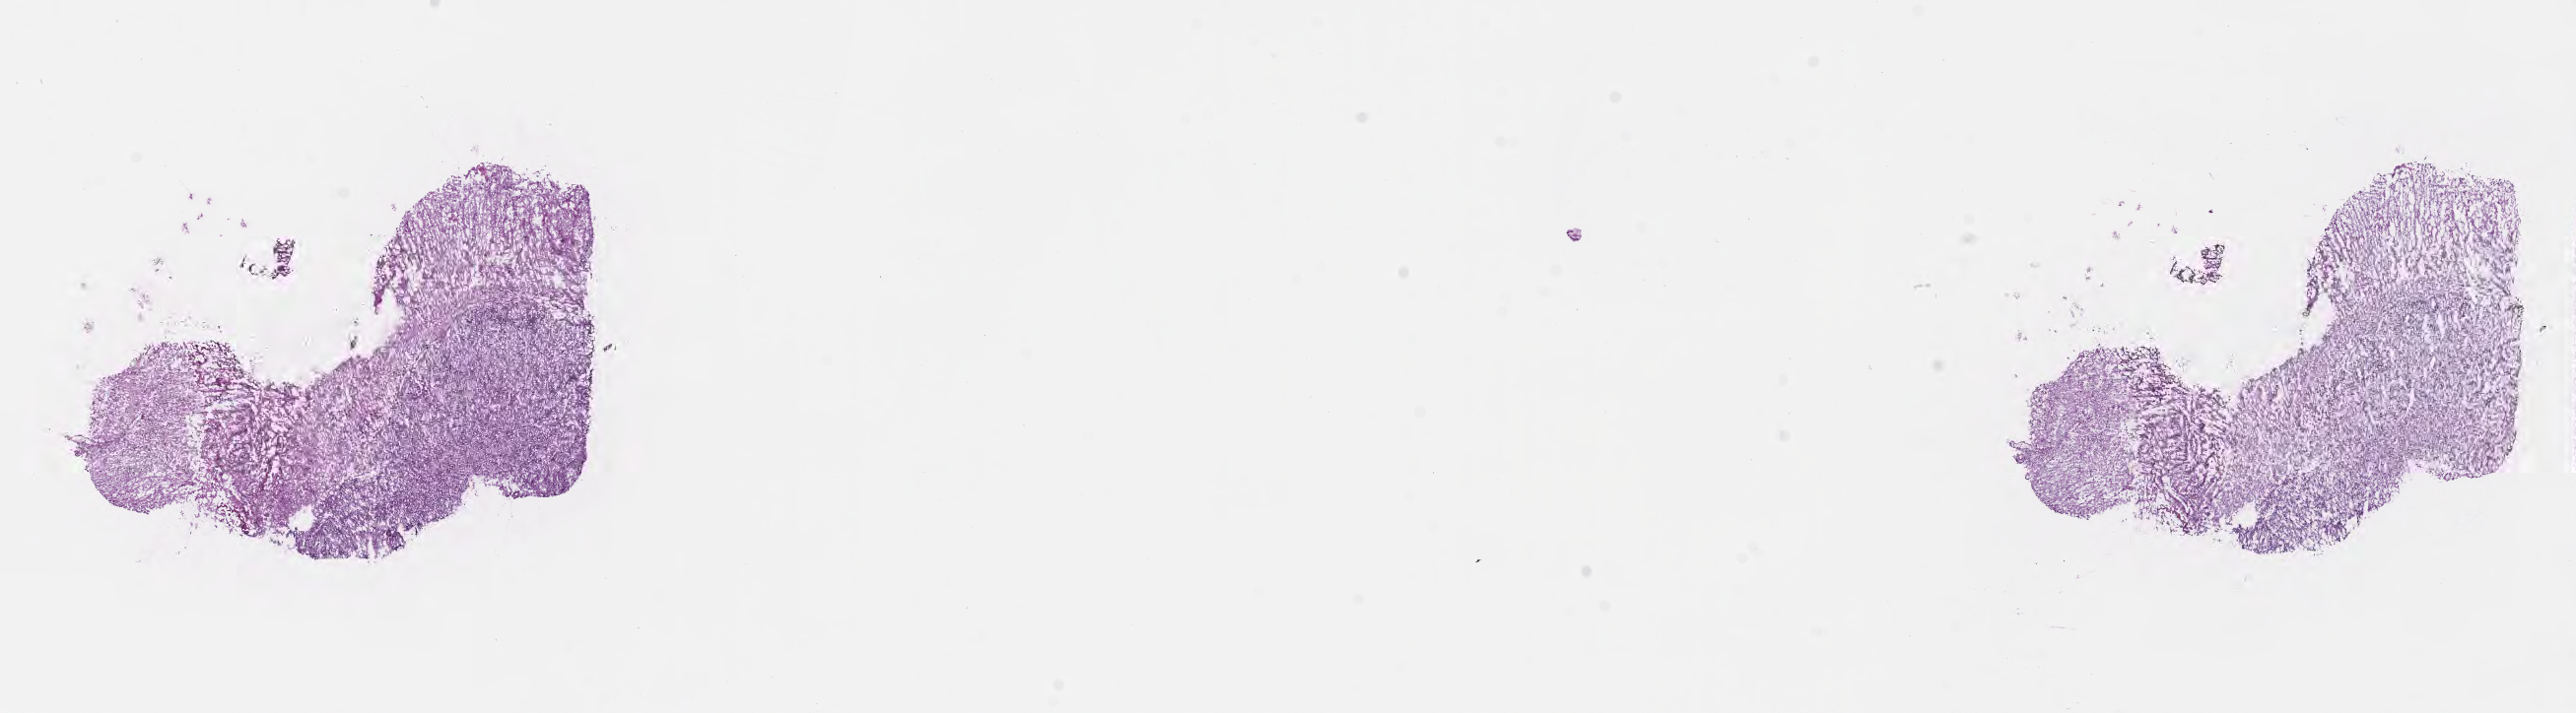
Haematoxylin and eosin whole-slide image, shown as a low-resolution overview of the whole scanned area (about 21.1 x 5.9 mm); frozen section (tissue freezing medium); specimen: recurrent tumor; anatomic site: brain. Female patient; age at initial diagnosis 53 years. Composition of this section per pathologist review: tumor cells 78%, tumor nuclei 88%, stromal cells 11%, necrosis 0%, normal cells 11%. Inflammatory infiltration, as recorded: lymphocyte infiltration 0%, monocyte infiltration 0%, neutrophil infiltration 0%.
* patient diagnosis: Glioblastoma, NOS
* section: top of the tissue portion